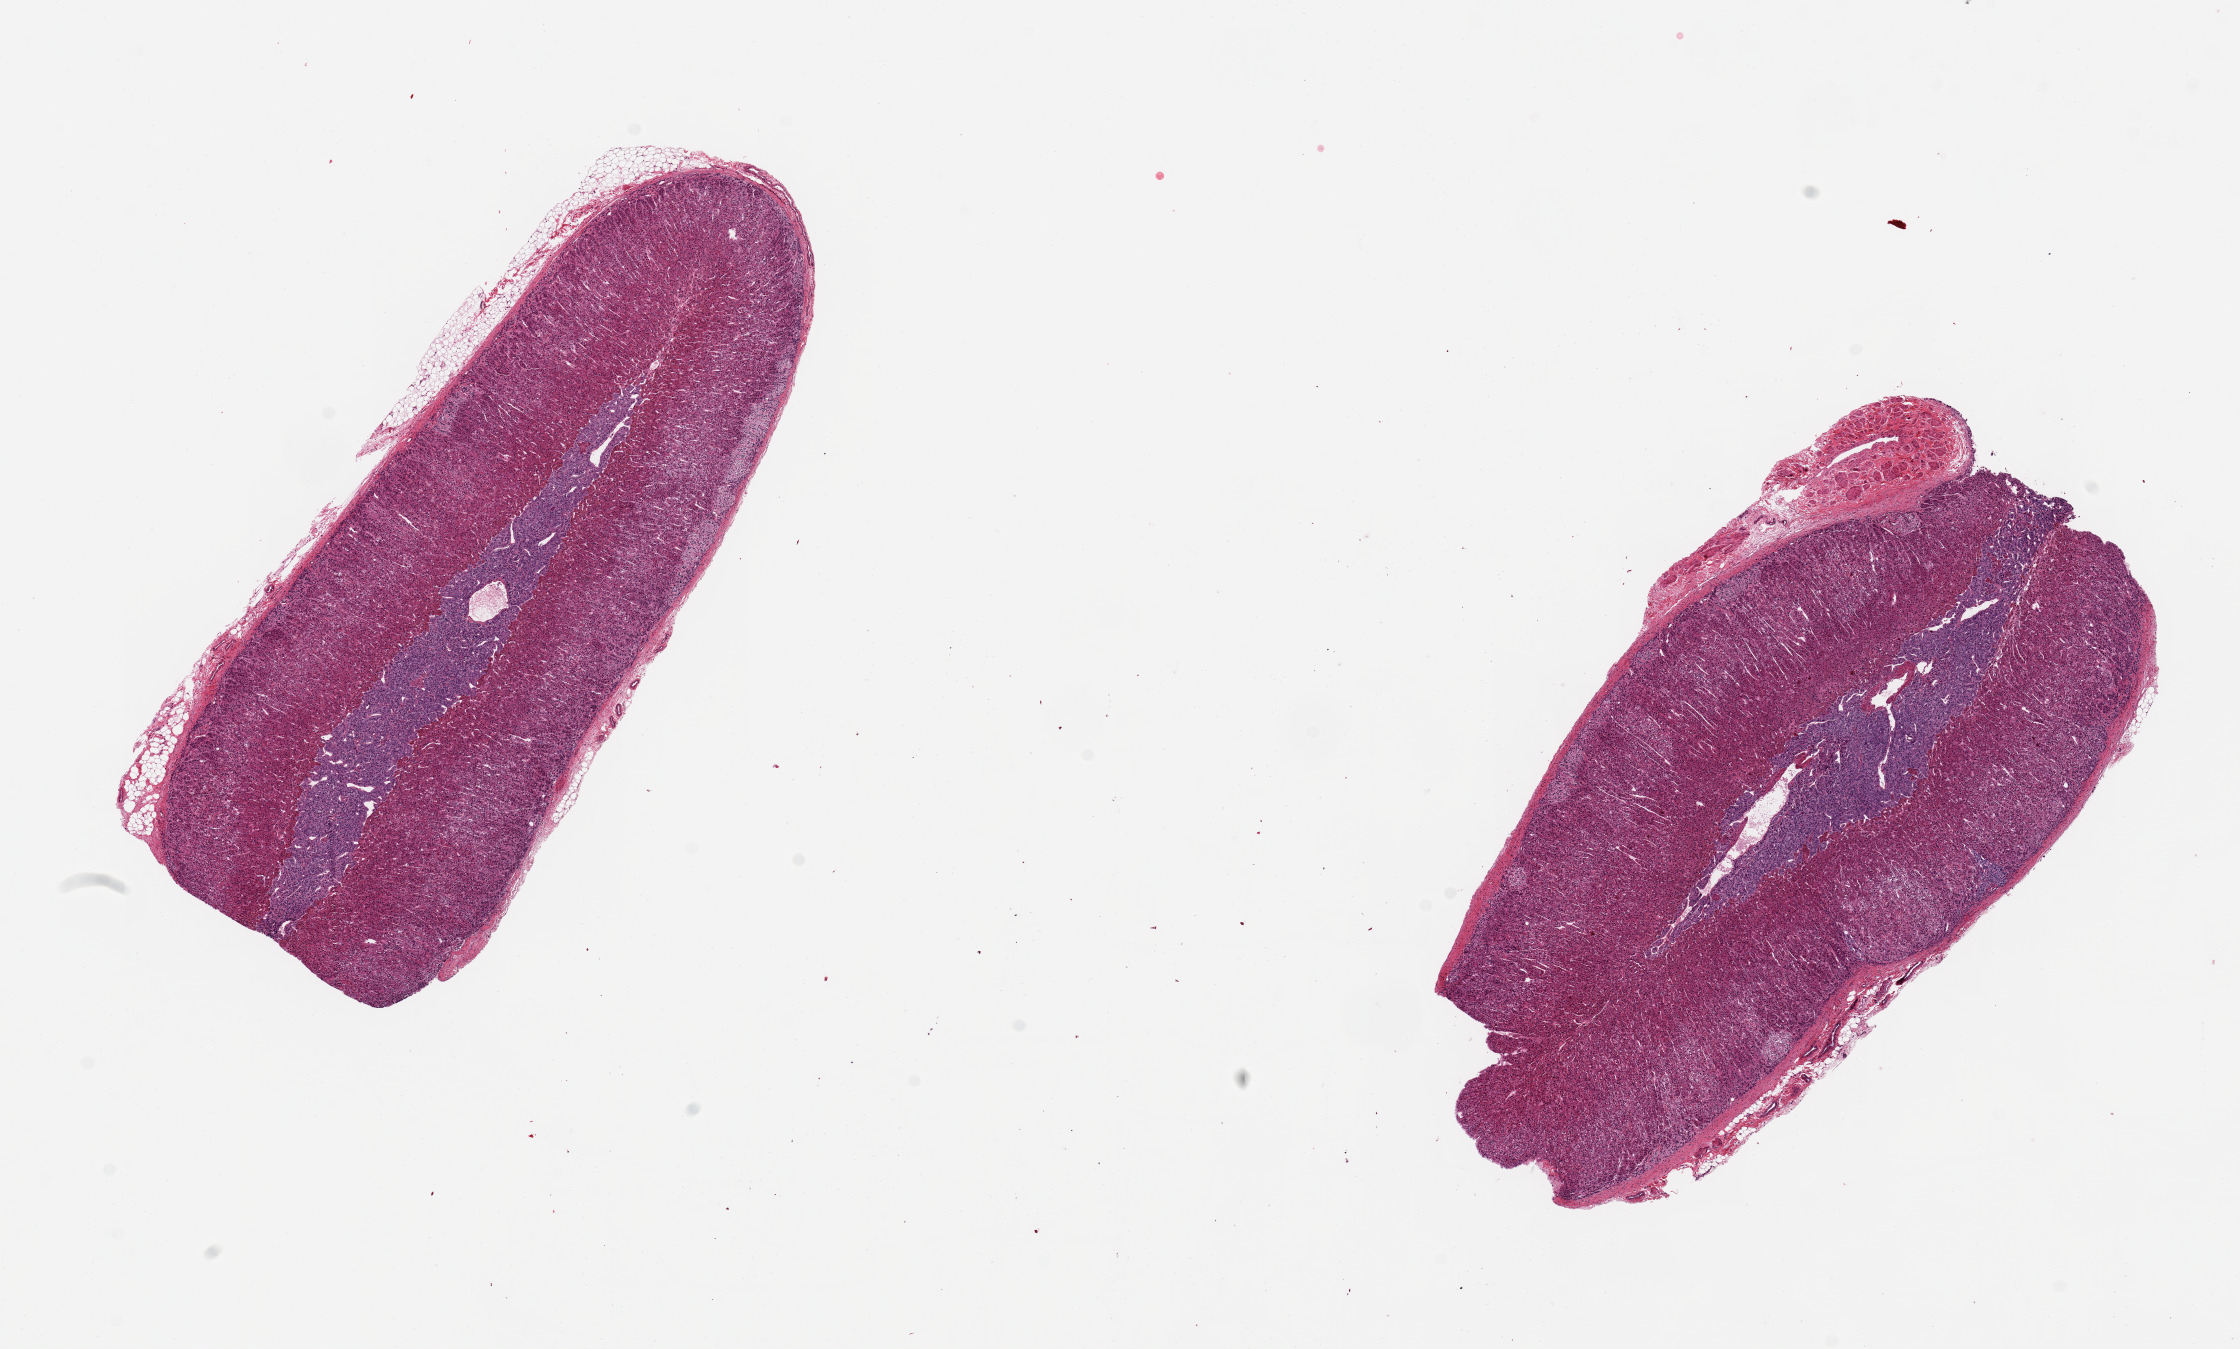
H&E whole-slide image, shown as a low-resolution overview of the whole scanned area (about 17.7 x 10.7 mm), PAXgene-fixed, paraffin-embedded tissue, sampled site (target tissue): adrenal gland, tissue donor sample. Donor sex: male.
• review note (as recorded): 2, ~3x7mm adrenal cortex and medulla, well preserved. 3x0.6mm attached nerve in one